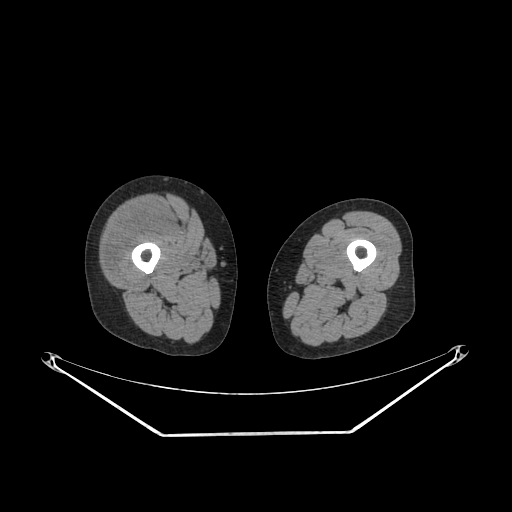
CT of an extremity soft-tissue mass (from a PET/CT study), one axial slice; slice 225 of 311 in the series (ordered by position); reconstruction kernel SOFT; soft-tissue window (W 400 / L 40 HU); 512 × 512 image matrix. Female patient. Case-level facts recorded for this patient, not image findings: histological type: pleiomorphic undifferentiated sarcoma; grade: high; site of the primary tumour: right quadricep.
Structures marked on this image (expert contour drawn on MRI and transferred to this co-registered scan by the dataset authors):
- tumour plus oedema (research contour): bounding box (x1, y1, x2, y2) in pixels: (105, 208, 165, 275)